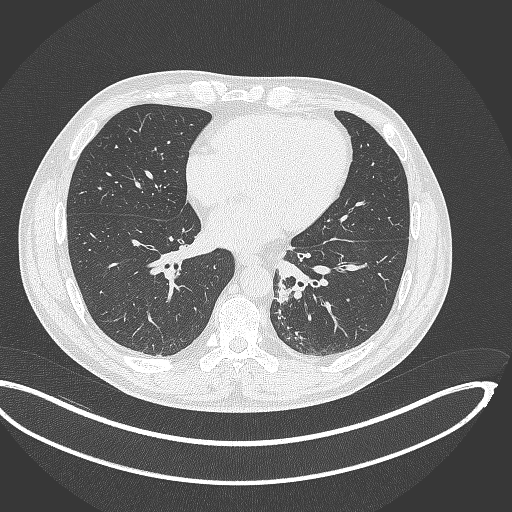
Chest CT, one axial slice; position 139 of 362 along the scan axis; 120 kVp; lung window (W 1500 / L -600 HU); 1 mm slice thickness; 512 × 512 image matrix, field of view 442 × 442 mm. Male patient, age 50 years. From the clinical record (not read from this slice): clinical TNM (as recorded): T2a N3 M0.
Annotated regions visible in this slice (bounding box drawn by a radiologist):
- lung tumour (recorded histology: squamous cell carcinoma): bounding box [x1, y1, x2, y2] px = [271, 277, 293, 307]